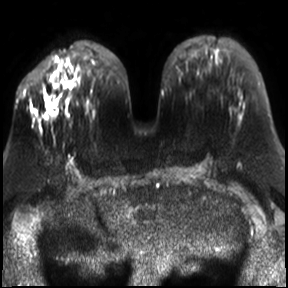
Breast MRI, one axial slice. Position 13 of 30 along the scan axis. Diffusion-weighted series; image 2 of 4 stored at this slice position (different b-values; order by instance number). 3 T. 4 mm slice thickness. 288 × 288 image matrix, field of view 340 × 340 mm. Female patient.
Outlined on this slice (outlined manually by an expert reader):
- tumour on diffusion-weighted imaging: bounding box <43,93,53,115> (left, top, right, bottom; pixels)